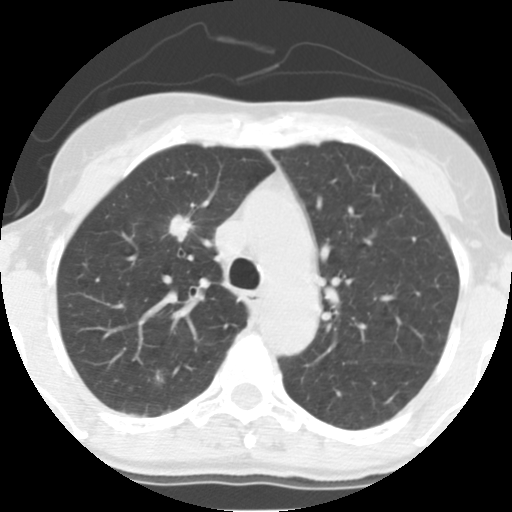
Axial slice from a low-dose chest CT screening exam; third annual screen; lung window (W 1500 / L -600 HU); 2.5 mm slice thickness; standard (soft-tissue) reconstruction kernel (STANDARD); slice 43 of 140 in the series. Female participant, aged 56 years at enrolment.
- Expert-annotated lung lesion, bounding box [x1, y1, x2, y2] px = [160, 209, 200, 249].
- Reader record for this screening exam (exam-level; its link to the box is not recorded): non-calcified nodule or mass ≥4 mm, right upper lobe, 17 × 12 mm, spiculated (stellate) margins, soft tissue attenuation, pre-existing on the prior screen: yes; interval growth: yes.